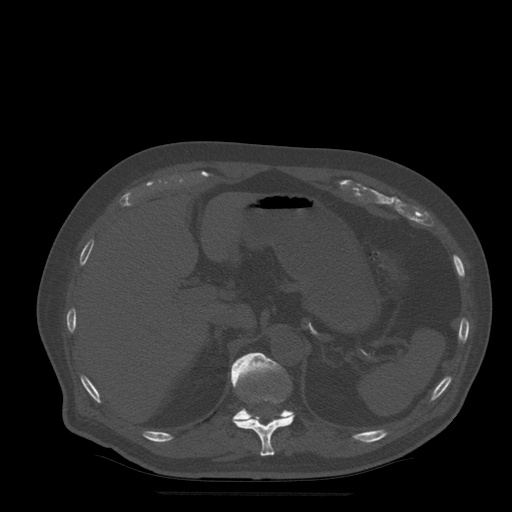
CT including the spine, one axial slice; bone window (W 1800 / L 400 HU); 1.25 mm slice thickness; 512 × 512 image matrix, field of view 420 × 420 mm. Patient age 72 years. Case-level facts recorded for this patient, not image findings: primary cancer: prostate.
Annotated regions visible in this slice (semi-automatic segmentation, software-assisted and operator-edited):
- T11 vertebra: bounding box <233,397,295,457> (left, top, right, bottom; pixels)
- T12 vertebra: <231,353,294,420>